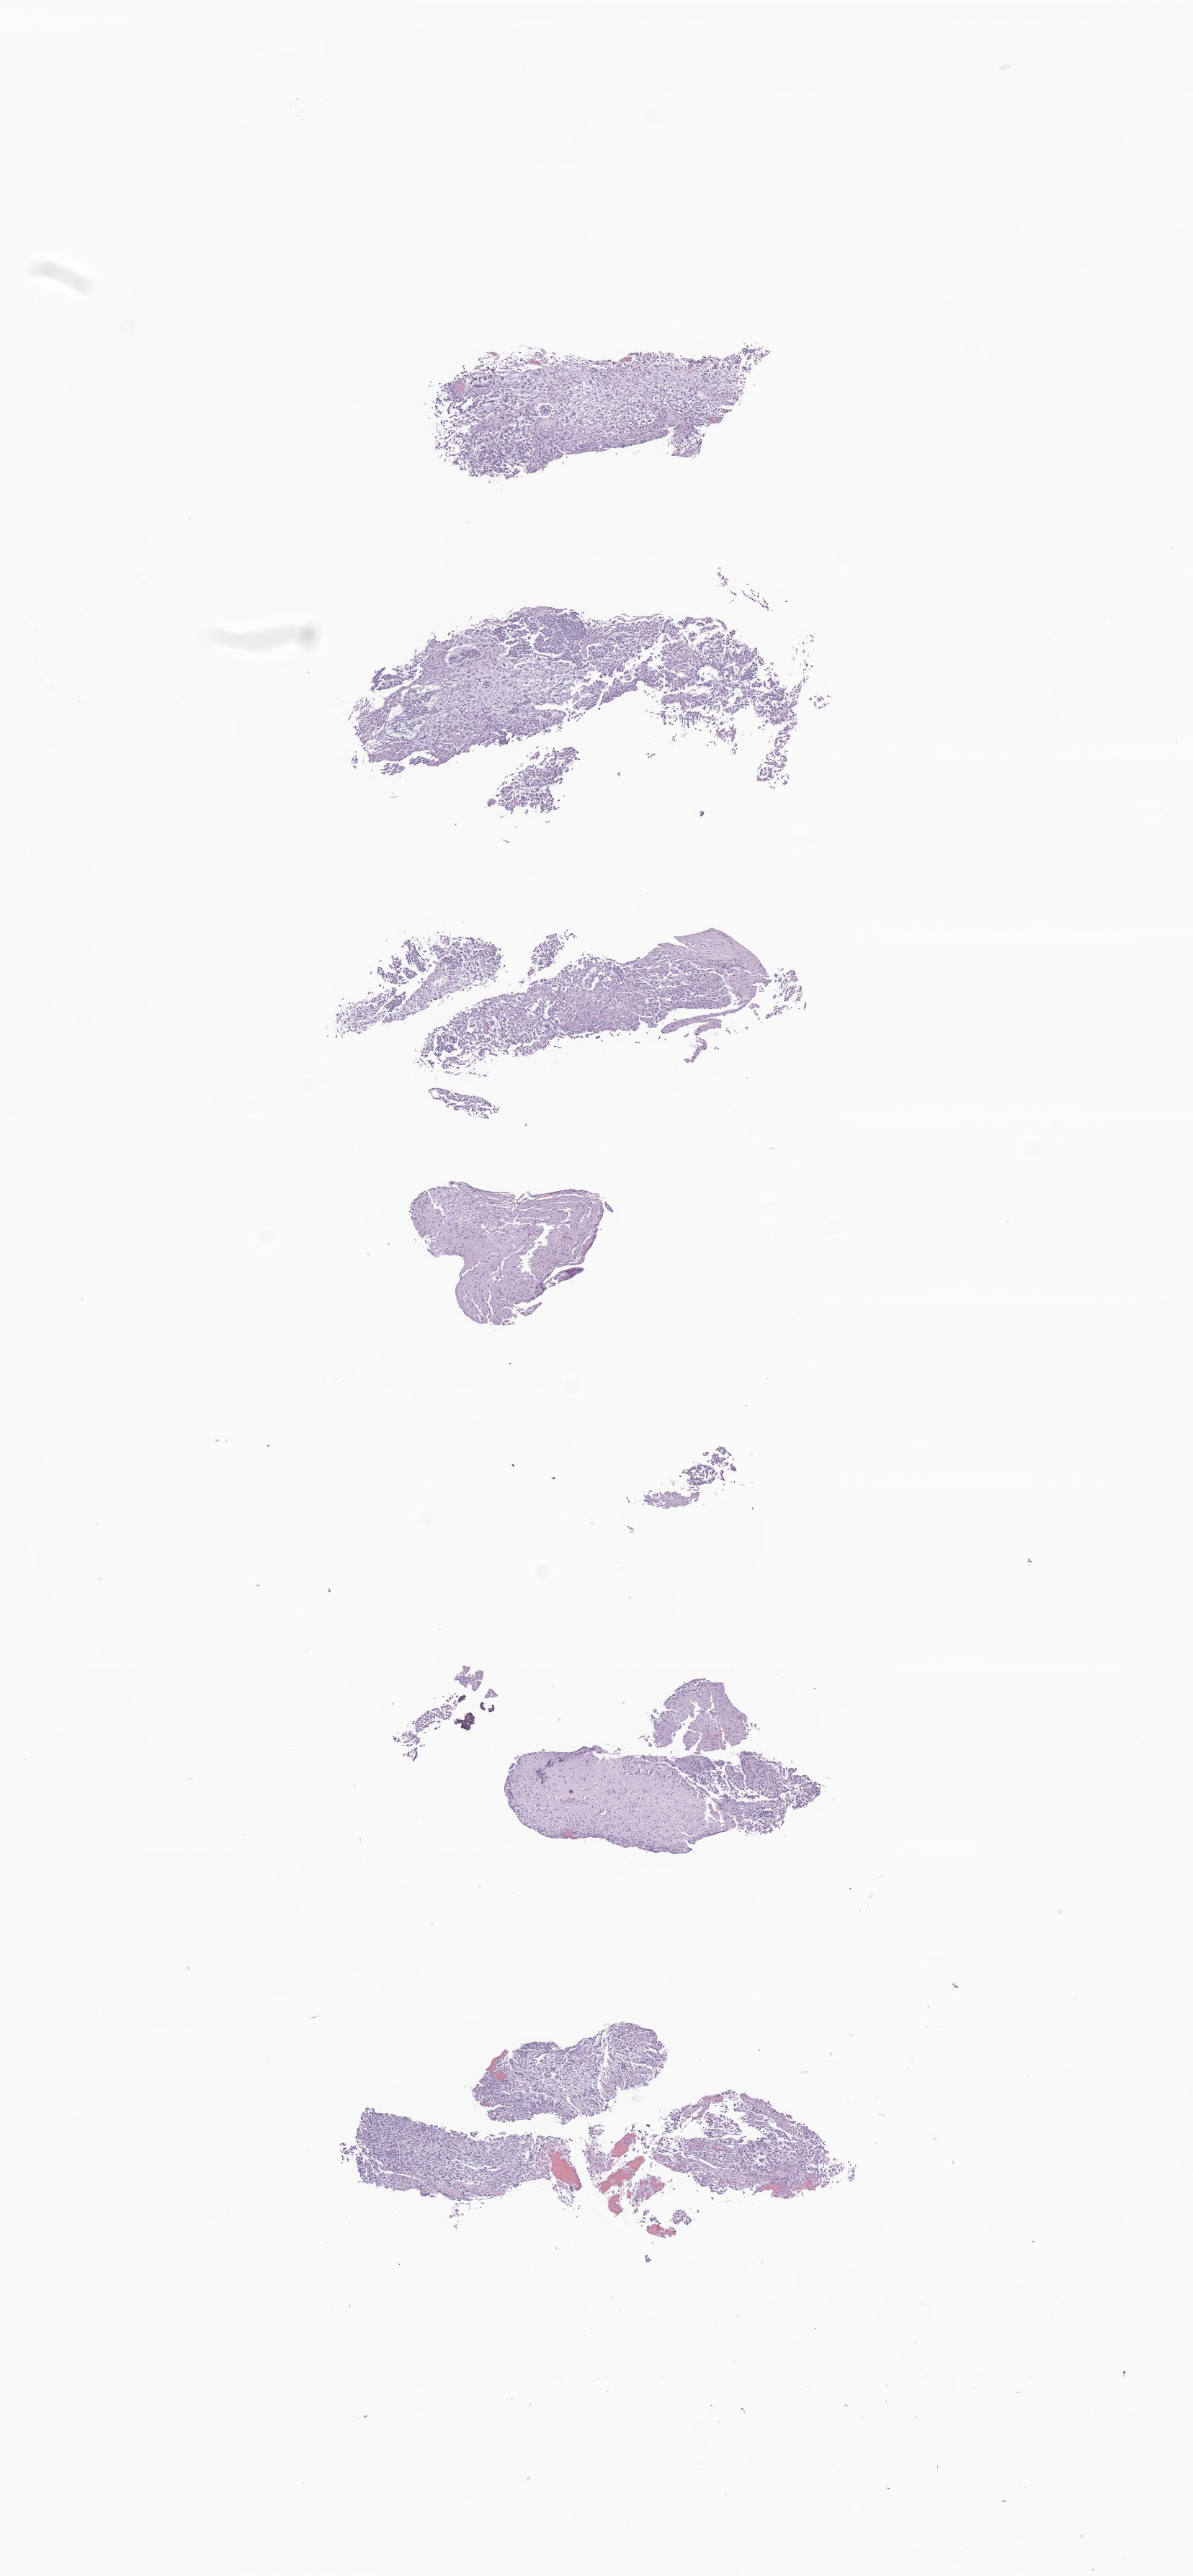
Haematoxylin and eosin whole-slide image of tumor tissue from the brain stem, low-resolution overview of the scanned area, about 7.0 x 15.1 mm; formalin-fixed paraffin-embedded section. Female patient, age 106 months (8 years 10 months).
- diagnosis (ICD-O-3 morphology term): Glioma, malignant